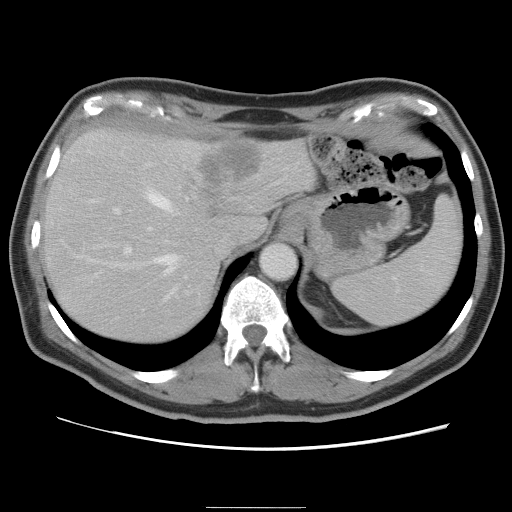
Contrast-enhanced abdominal CT, one axial slice. Position 62 of 87 along the scan axis. Intravenous contrast given. Soft-tissue window (W 400 / L 40 HU). 5 mm slice thickness. 512 × 512 image matrix, field of view 363 × 363 mm. Male patient, age 63 years. From the clinical record (not read from this slice): diagnosis: colorectal cancer liver metastases, imaged before liver resection; multiple liver metastases: no; largest metastasis: 9 cm.
Annotated regions visible in this slice (outlined manually by an expert reader):
- hepatic veins: box from (x=96, y=184) to (x=187, y=300) px
- liver: (x=42, y=128)–(x=314, y=345)
- planned liver remnant (the part of the liver to remain after resection): (x=42, y=158)–(x=220, y=345)
- portal vein (with intrahepatic branches): (x=96, y=207)–(x=188, y=293)
- liver metastasis: (x=202, y=143)–(x=259, y=186)